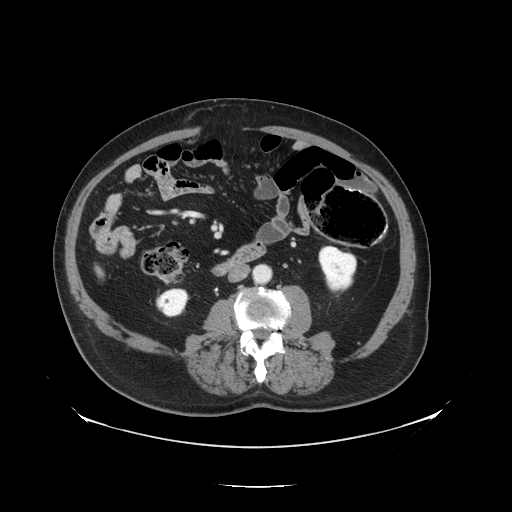
Contrast-enhanced abdominal CT, one axial slice. Position 29 of 138 along the scan axis. Reconstruction kernel STANDARD. 120 kVp. Intravenous contrast given. Soft-tissue window (W 400 / L 40 HU). 2.5 mm slice thickness. 512 × 512 image matrix, field of view 497 × 497 mm. Male patient, age 77 years. Case-level facts recorded for this patient, not image findings: diagnosis: colorectal cancer liver metastases, imaged before liver resection; multiple liver metastases: no; largest metastasis: 1.5 cm.
Structures marked on this image (manually delineated by an expert):
- liver: bounding box [x1, y1, x2, y2] px = [97, 268, 104, 277]
- planned liver remnant (the part of the liver to remain after resection): [98, 268, 102, 270]